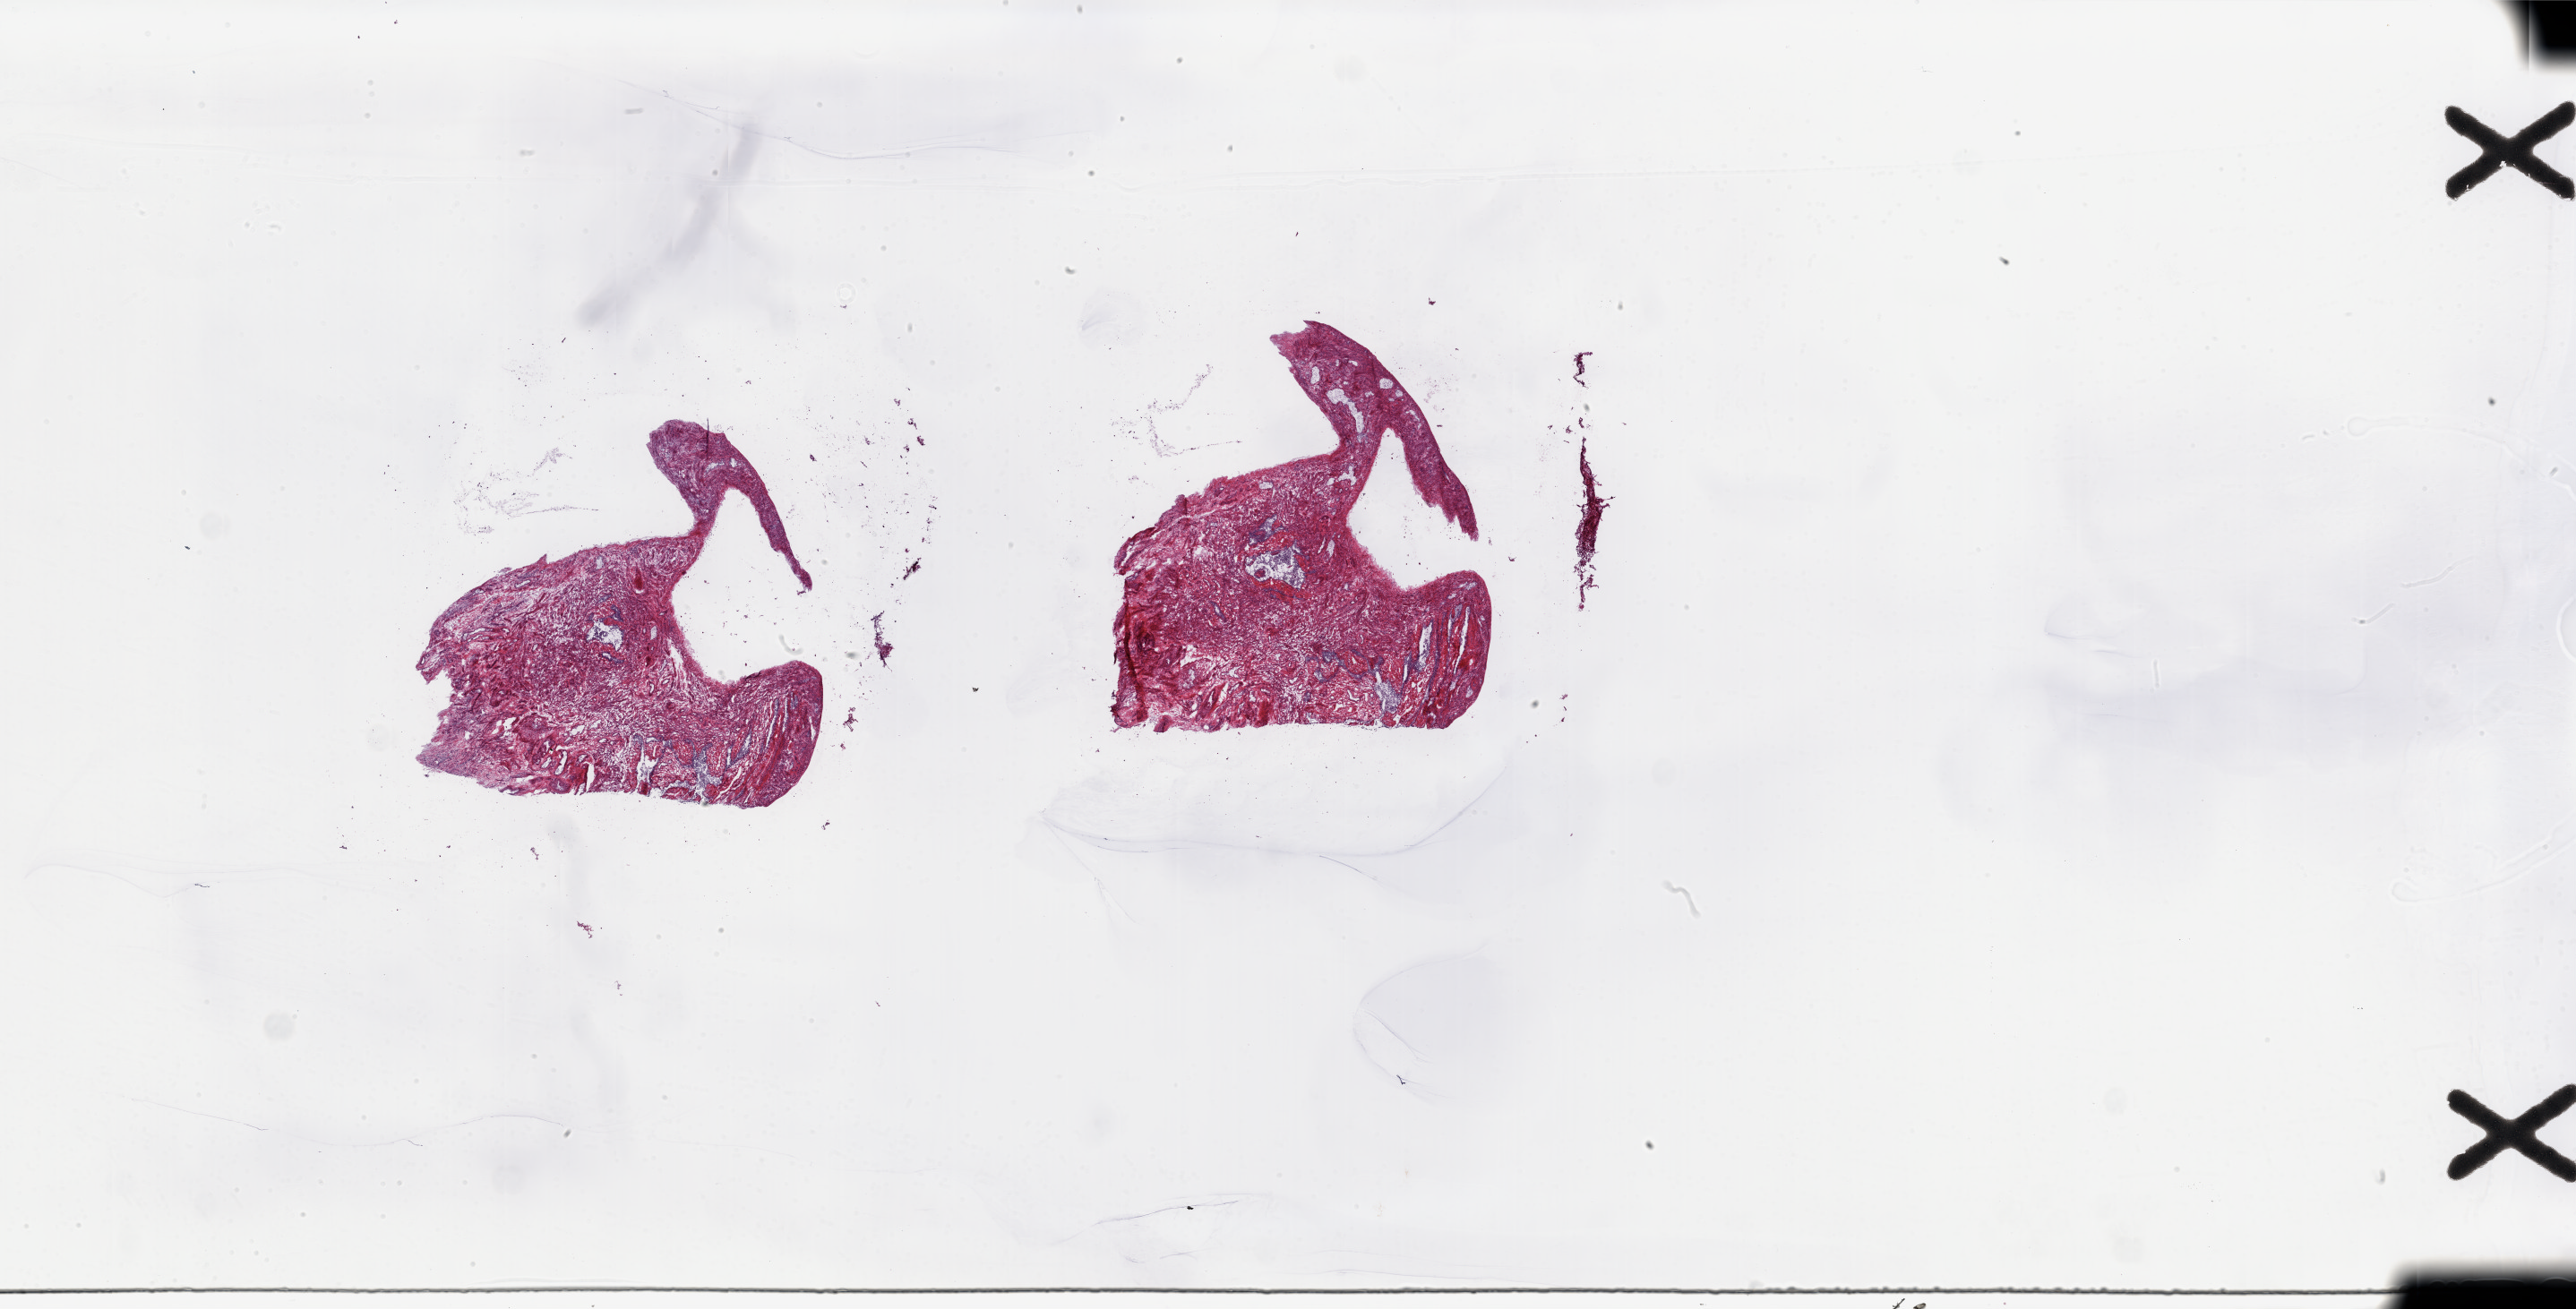
Digitized Hematoxylin and eosin (H&E) stained tissue section (whole slide), a low-resolution overview of the entire scanned area, about 45.6 x 23.2 mm (slide scanned at 20x); frozen section; sample: solid tissue normal (non-tumour tissue), uterus. Female, age 61 years at initial diagnosis.
This section: solid tissue normal (non-tumour) sample from the same patient. Patient diagnosis: Endometrioid adenocarcinoma, NOS (endometrium).